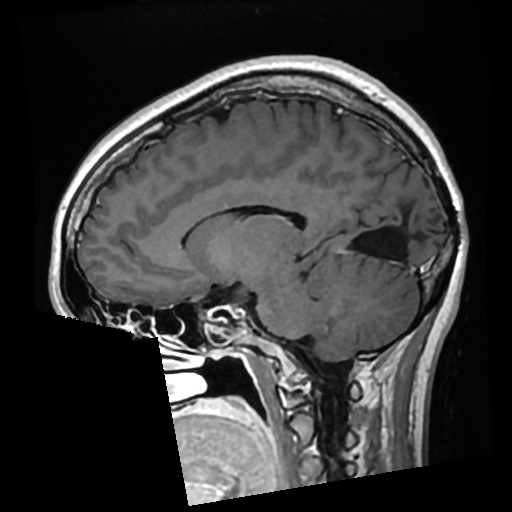
Brain MRI from a brain-tumour surgery series, one sagittal slice; slice 124 of 276 in the series (ordered by position); T1-weighted post-contrast; 0.7 mm slice thickness; 512 × 512 image matrix, field of view 250 × 250 mm. Case-level facts recorded for this patient, not image findings: histopathology: Glioma with ependymal features; WHO grade: 2; tumour location: Left Parietal.
Outlined on this slice (expert manual segmentation):
- previous resection cavity: bounding box (x1, y1, x2, y2) in pixels: (386, 241, 402, 258)